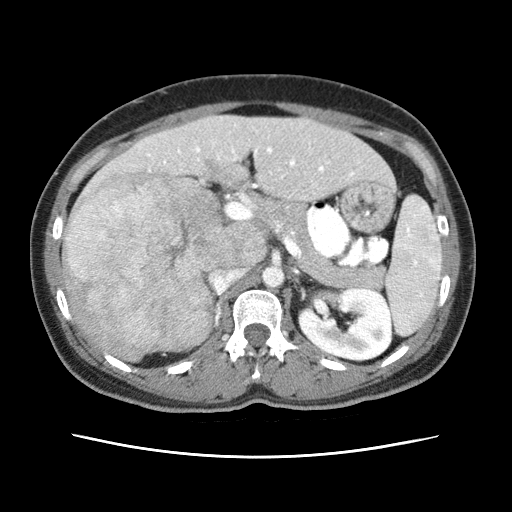
Contrast-enhanced abdominal CT (liver protocol), one axial slice; reconstruction kernel STANDARD; 120 kVp; soft-tissue window (W 400 / L 40 HU); 512 × 512 image matrix, field of view 340 × 340 mm. From the clinical record (not read from this slice): diagnosis: hepatocellular carcinoma (patient treated with transarterial chemoembolisation; whether this scan precedes or follows treatment is not stated here); TNM stage (as recorded): Stage-I; Child-Pugh class: A; tumour nodularity: uninodular.
Annotated regions visible in this slice (semi-automatically segmented with operator editing):
- abdominal aorta: bounding box <263,268,285,288> (left, top, right, bottom; pixels)
- liver parenchyma outside the tumour (the mass and vessels are separate outlines, so this box may not span the whole liver): <62,114,388,360>
- mass: <63,169,231,359>
- liver vessels: <148,147,354,175>